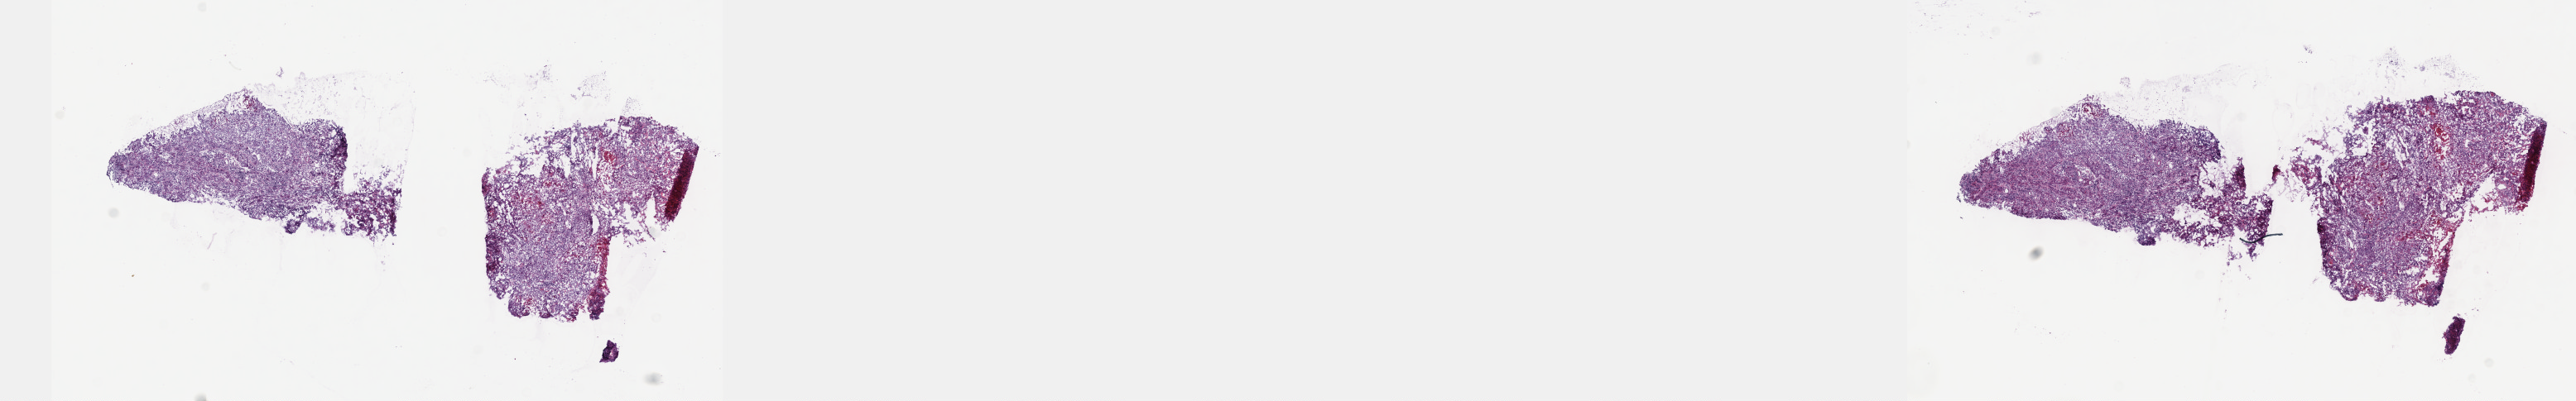
Whole-slide histology image, H&E-stained — low-resolution overview of the scanned area, about 25.1 x 3.9 mm; frozen section from the top of the tissue portion; cervix, primary tumour sample. Female patient; age at initial diagnosis 53 years. Histologic grade: GX (grade cannot be assessed). Composition of this section per pathologist review: tumour cells 75%, tumour nuclei 90%, normal cells 0%, stromal cells 25%, necrosis 0%. Infiltration values recorded for this section: lymphocyte infiltration 0%, monocyte infiltration 0%, neutrophil infiltration 0%.
Diagnosis: Squamous cell carcinoma, NOS (cervix uteri). FIGO stage: IVA.